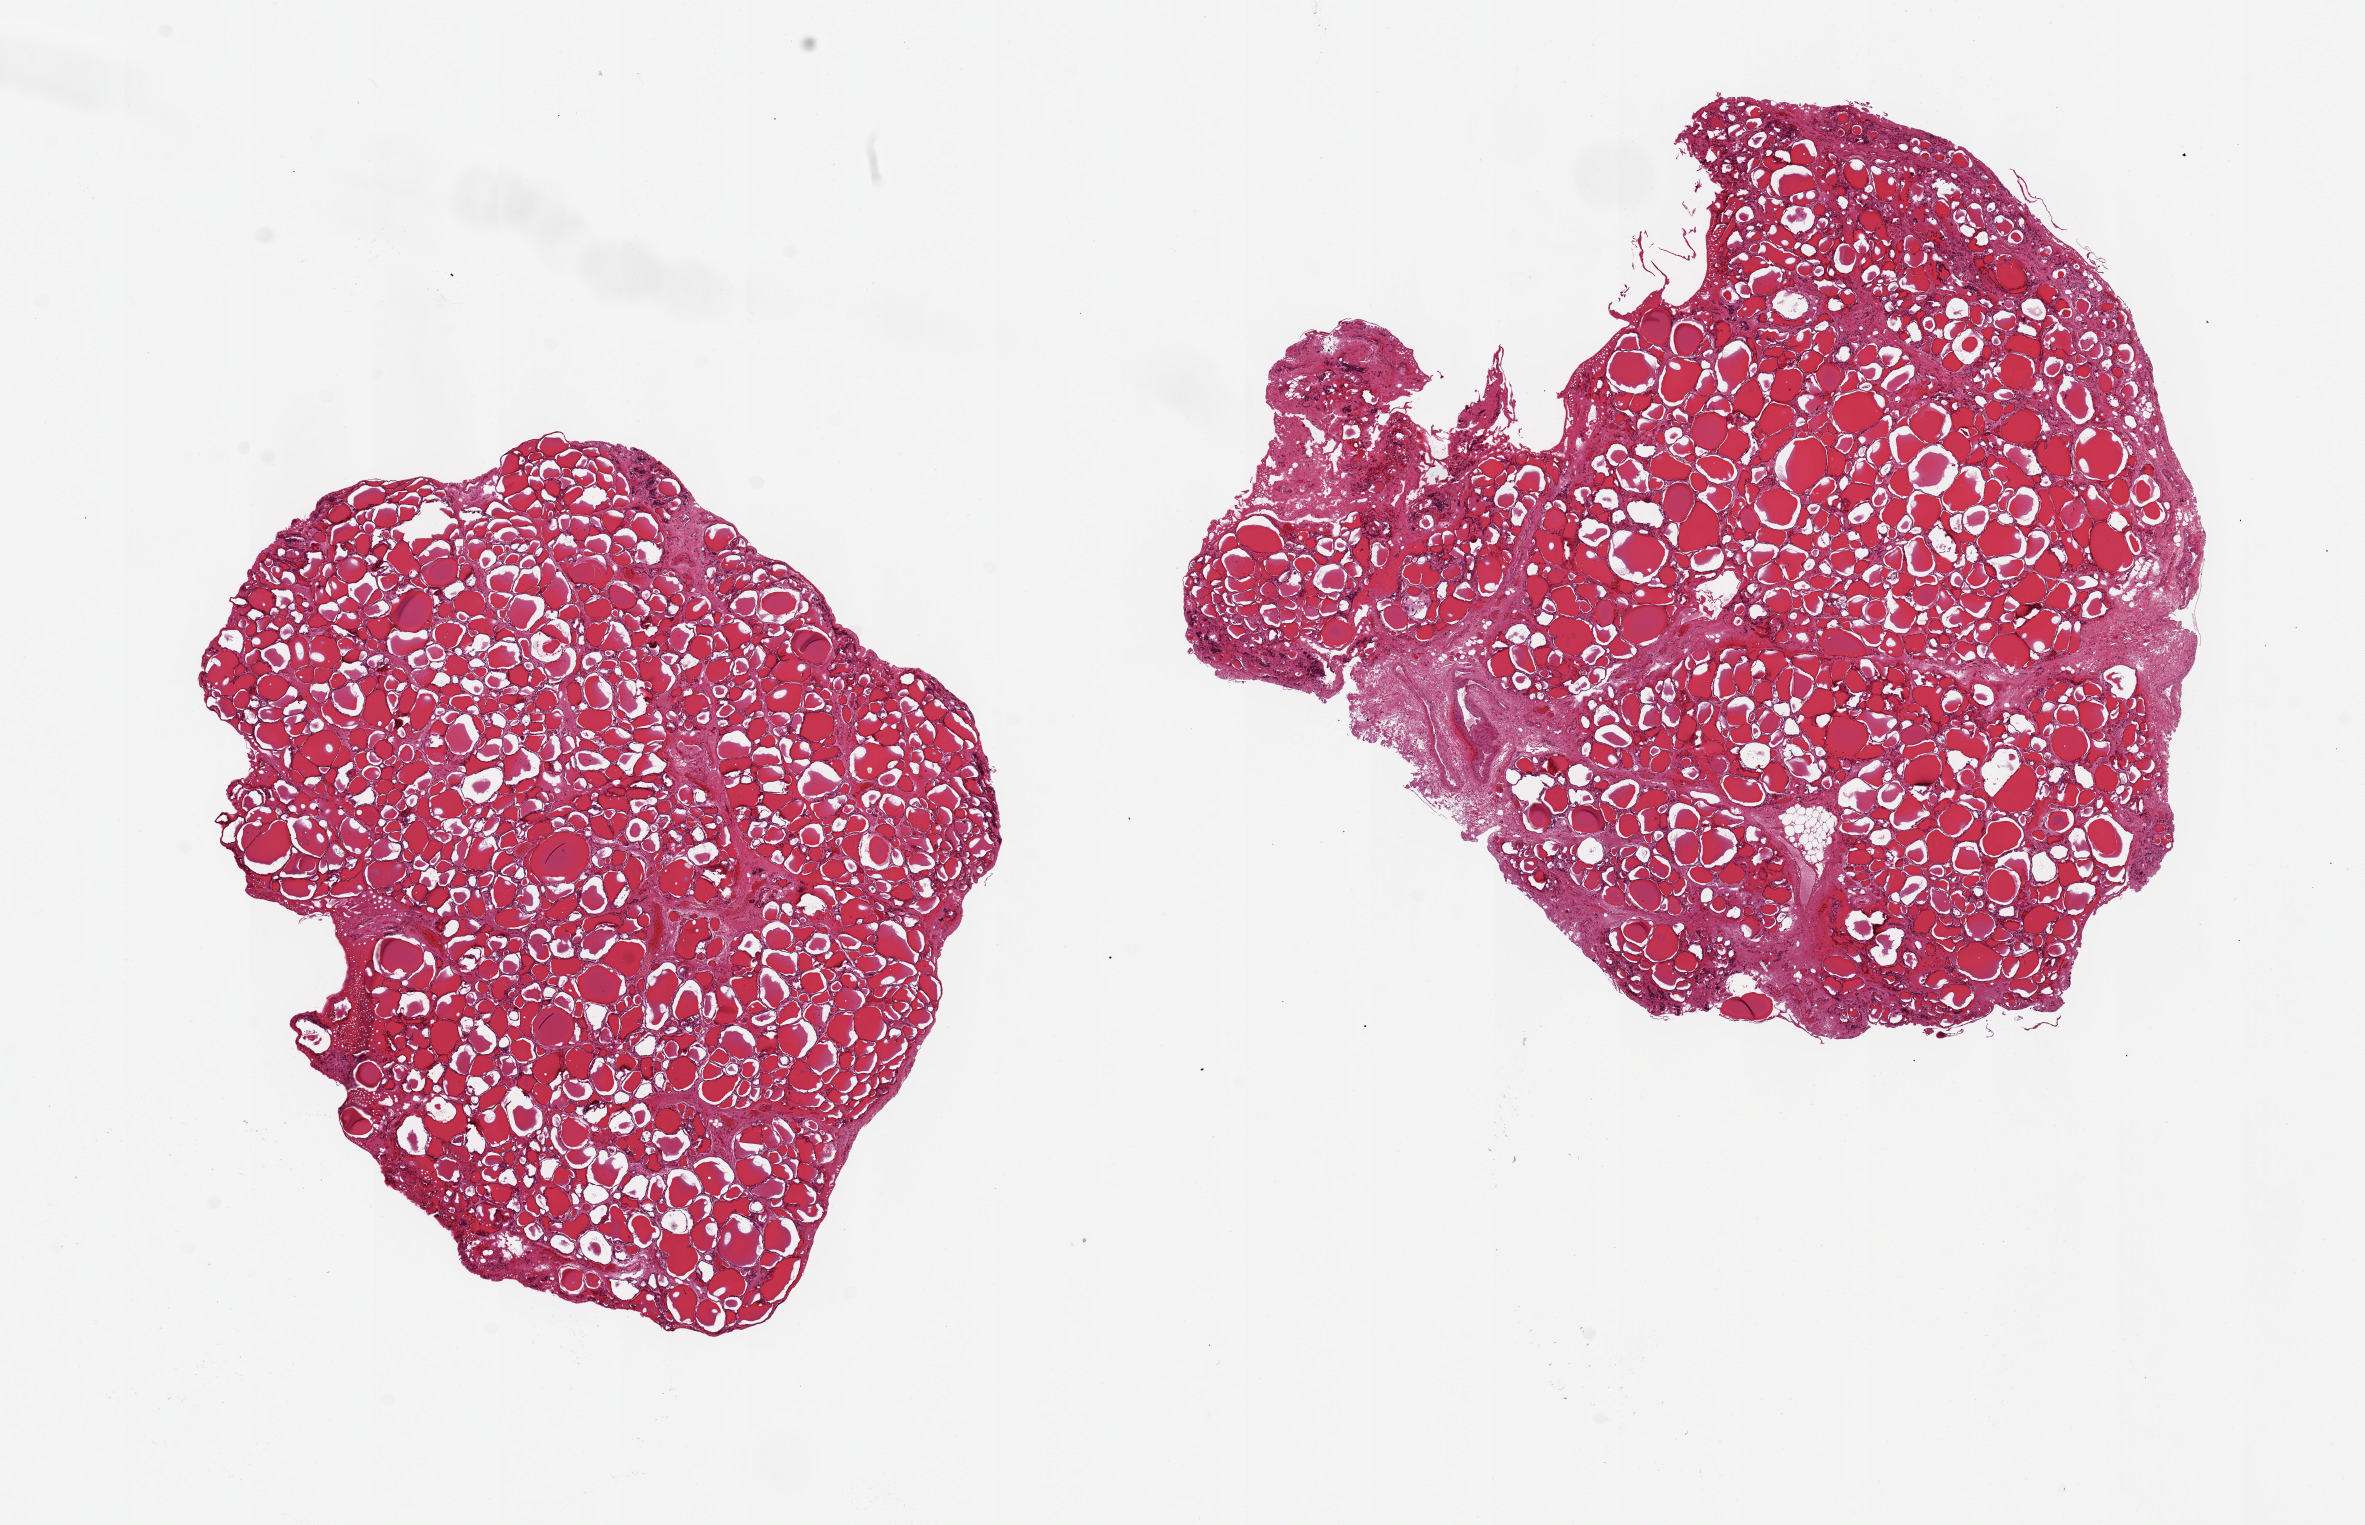
Digitized haematoxylin and eosin-stained section, brightfield, whole scanned area (about 18.7 x 12.1 mm, from a 20x scan) shown as a low-resolution overview; PAXgene-fixed, paraffin-embedded tissue; section of thyroid (target tissue); donor tissue sample.
Review note (as recorded): 2 pieces, 7x5 & 8x7mm.